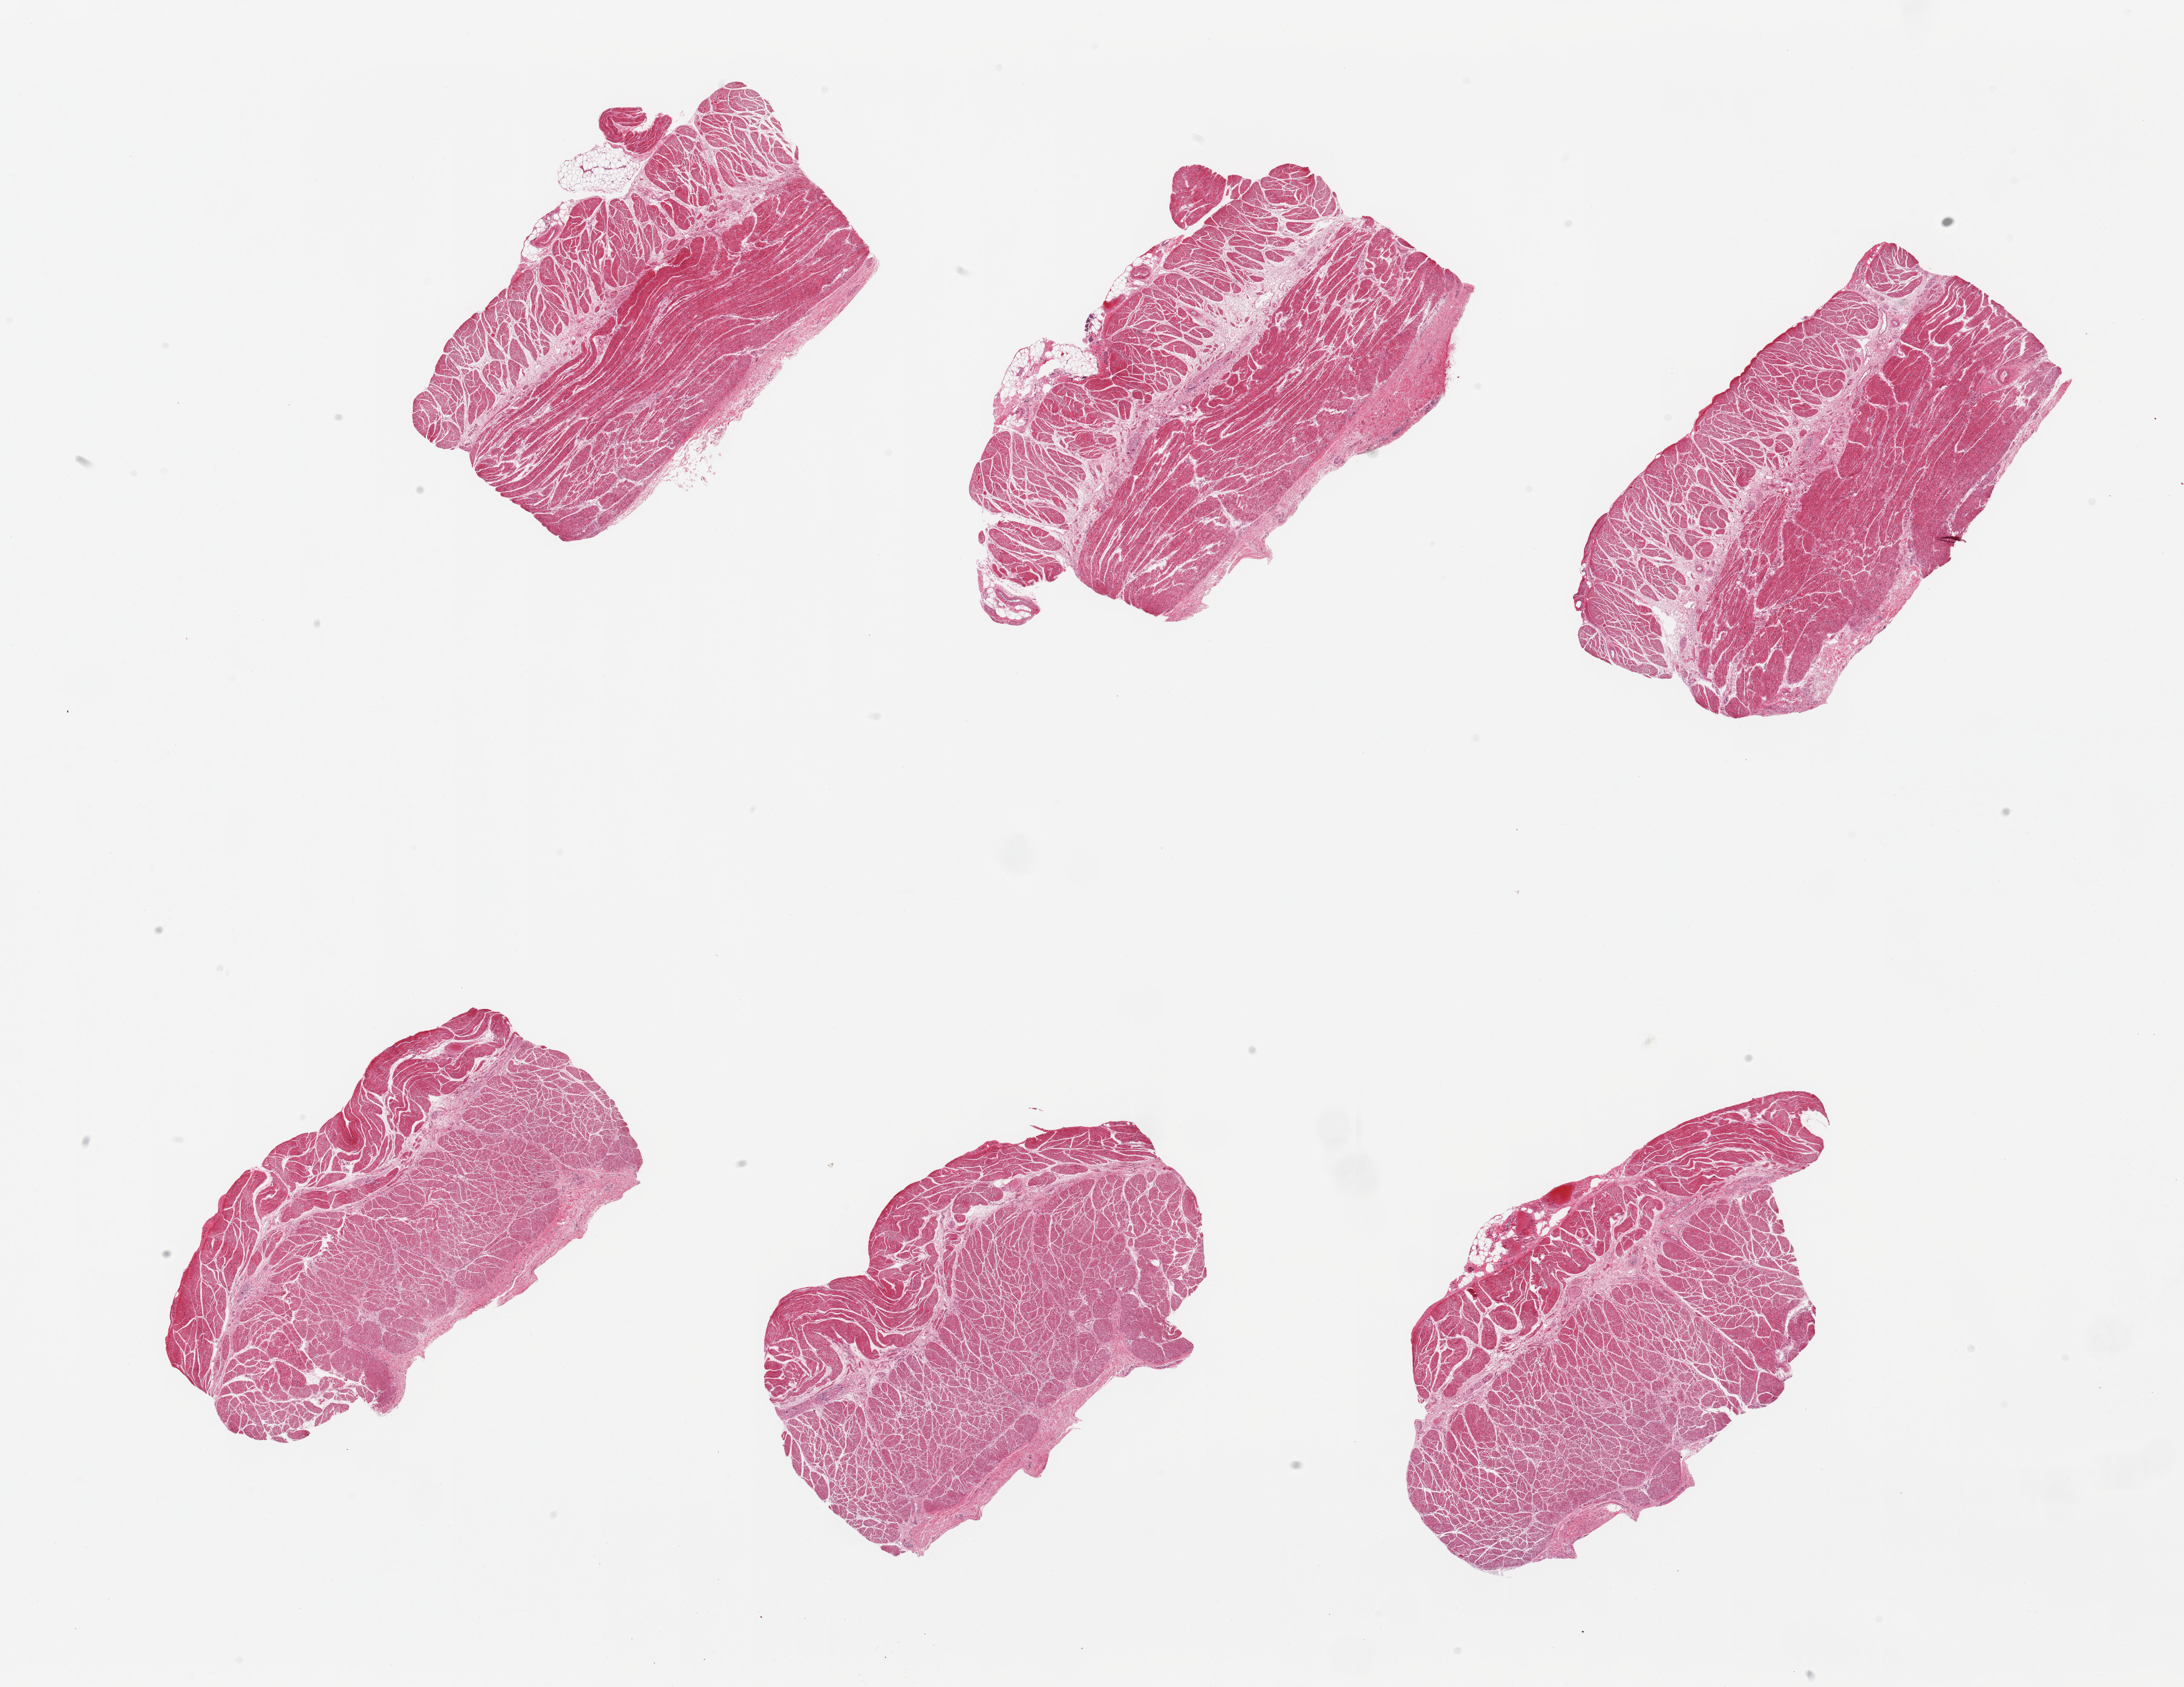
Whole-slide image, hematoxylin and eosin (H&E) stain, brightfield — whole scanned area (about 28.5 x 22.1 mm, from a 20x scan) shown as a low-resolution overview. PAXgene-fixed paraffin-embedded (PFPE) section. Sampled site (target tissue): esophageal muscle. Donor tissue sample.
Pathologist's review note for this sample: 6 pieces, confirmed target muscularis.